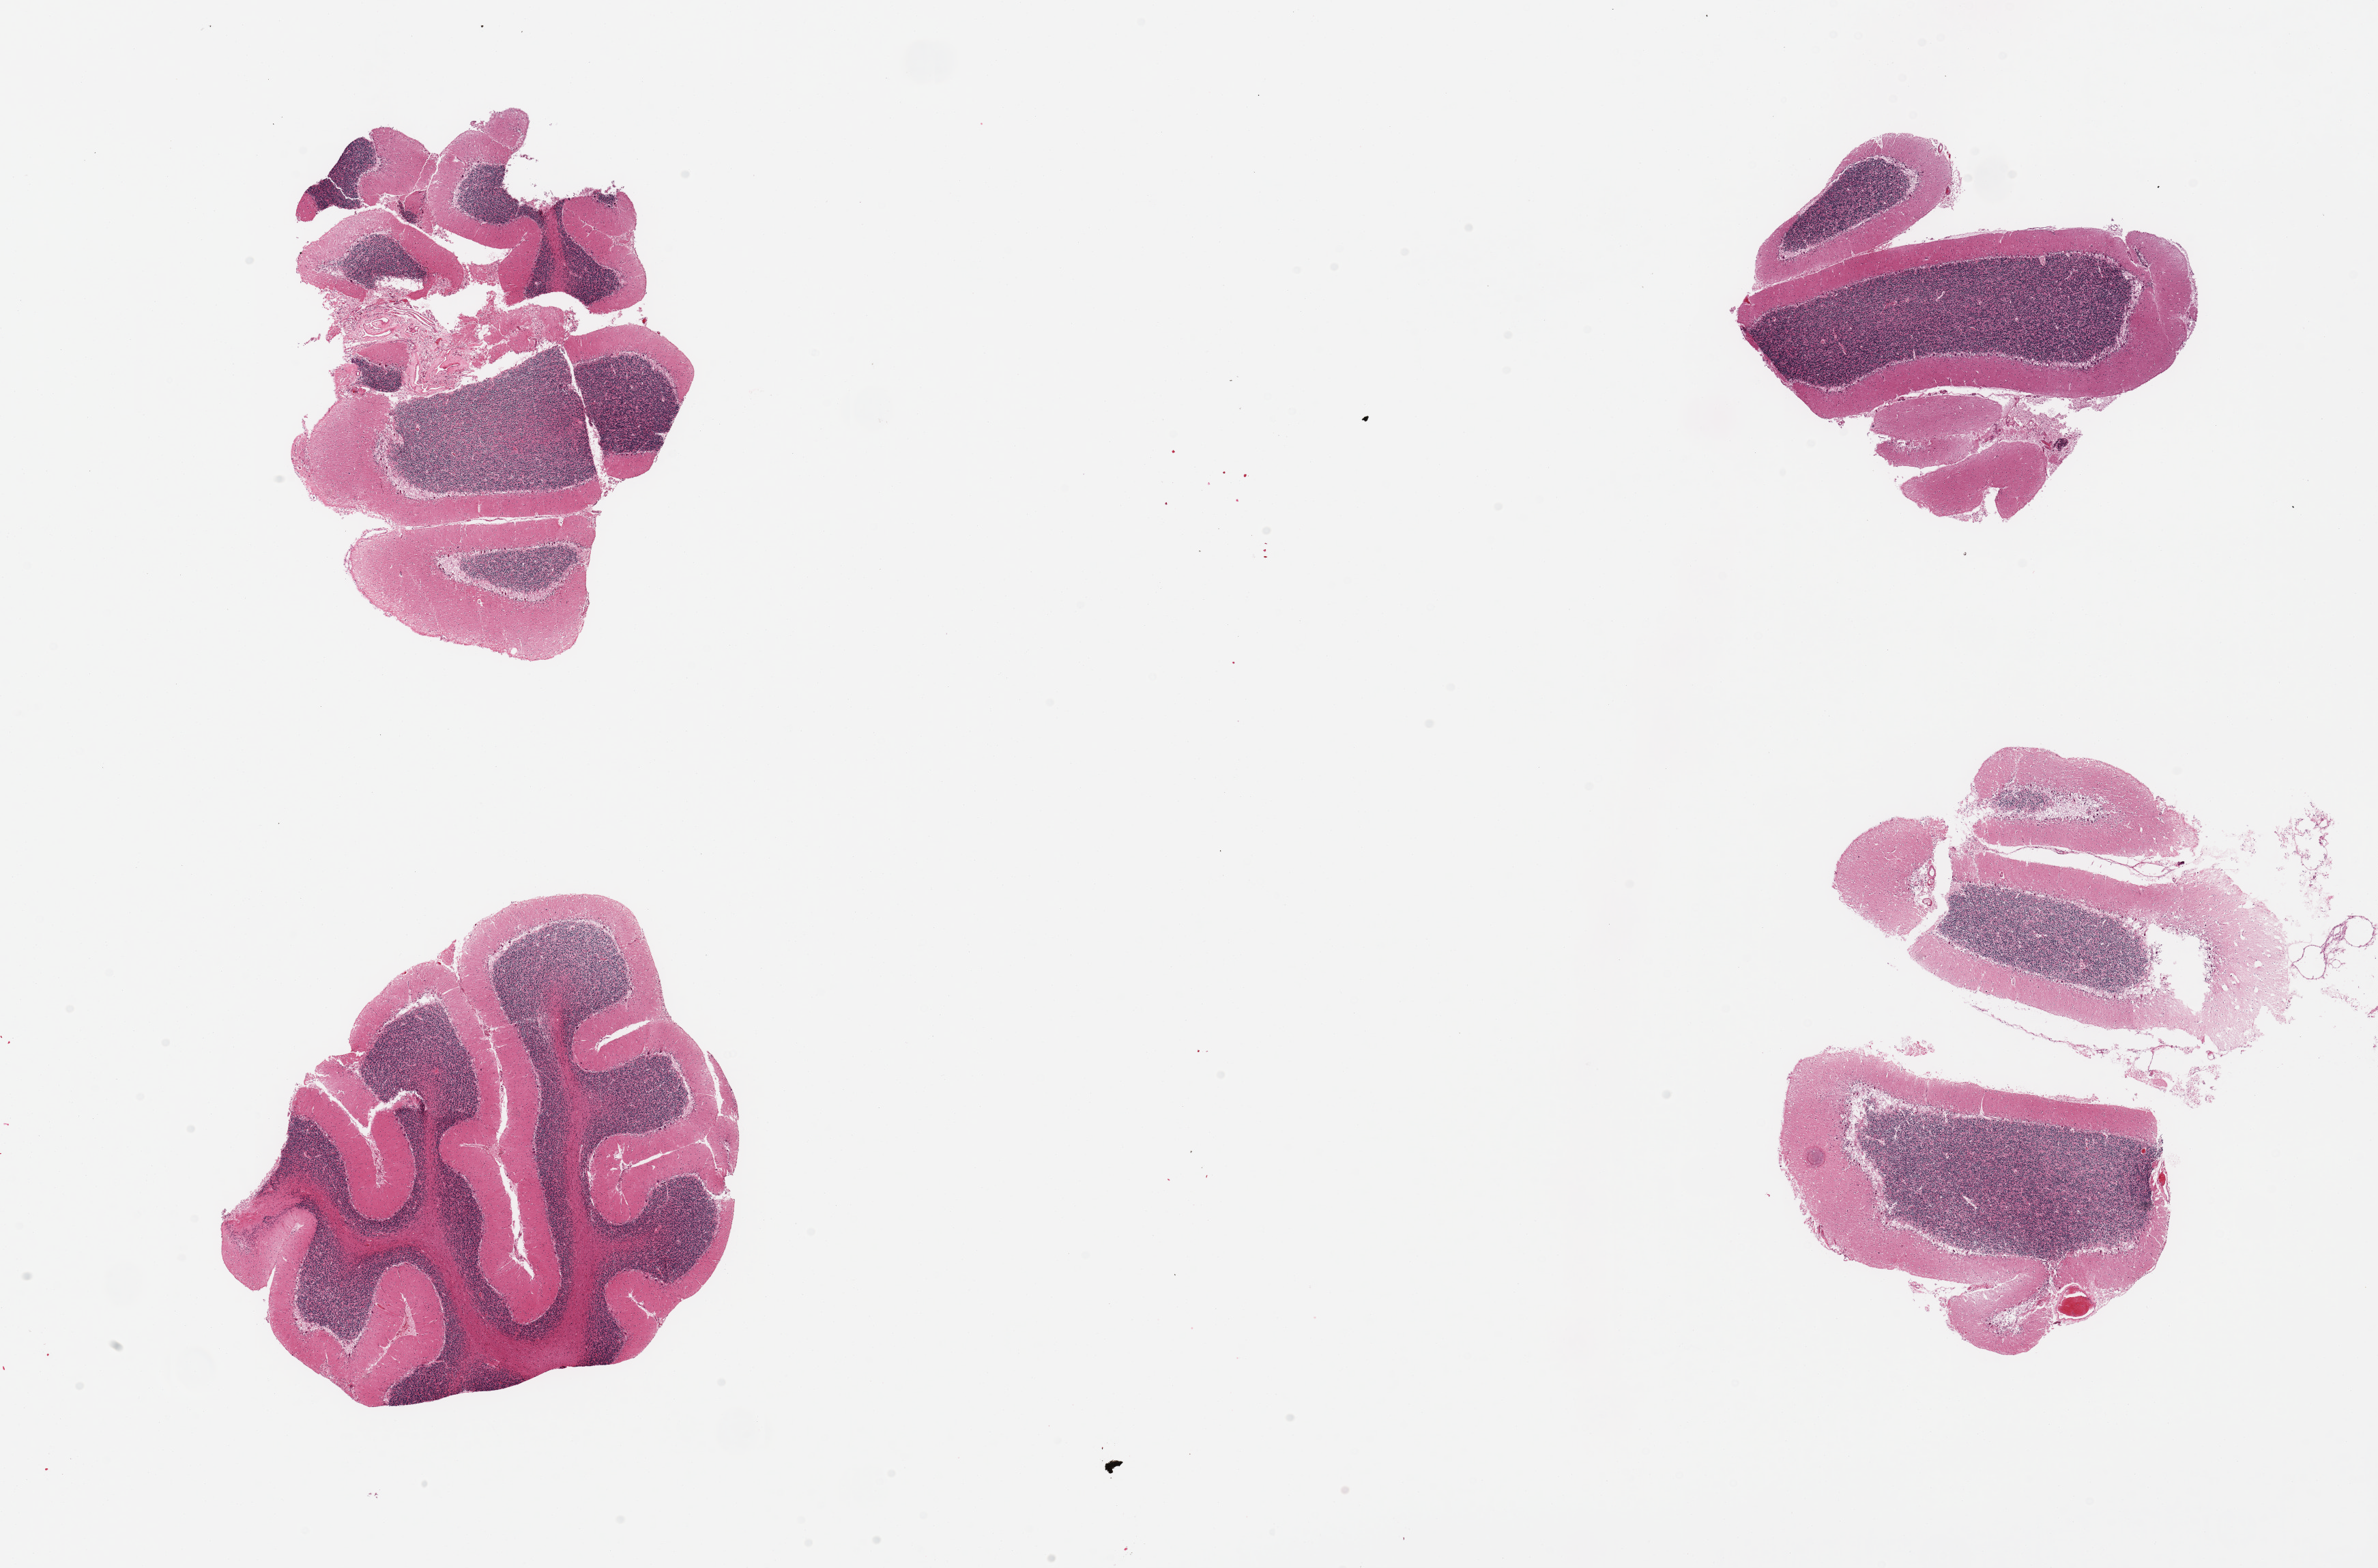
Hematoxylin and eosin (H&E) whole-slide image — whole scanned area (about 27.6 x 18.2 mm) shown as a low-resolution overview, PAXgene-fixed paraffin-embedded (PFPE) section, sampled site (target tissue): cerebellum, donor tissue sample. Donor sex: female.
Reviewer comment on this tissue sample: 4 pieces; foci of adherent meninges; autolysis varies from 1 to 2.